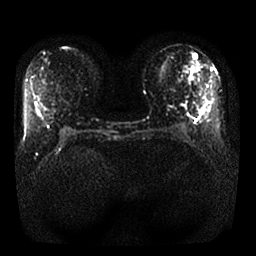
Breast MRI, one axial slice; slice 10 of 25 in the series (ordered by position); diffusion-weighted series; image 2 of 4 stored at this slice position (different b-values; order by instance number); 1.5 T; 4 mm slice thickness; 256 × 256 image matrix, field of view 340 × 340 mm. Female patient.
Structures marked on this image (outlined manually by an expert reader):
- tumour on diffusion-weighted imaging: bounding box [x1, y1, x2, y2] px = [188, 77, 192, 83]